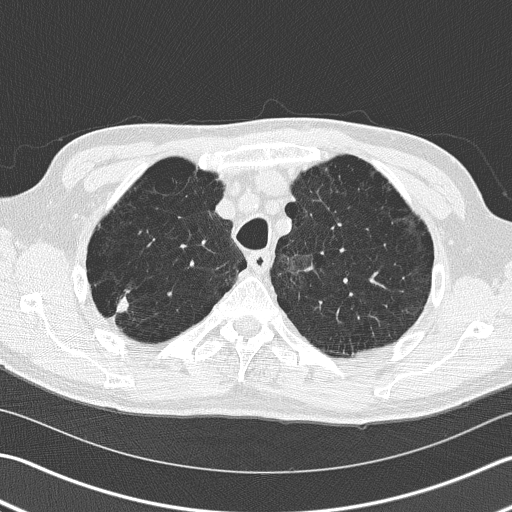
Low-dose screening chest CT, one axial slice. Slice 127 of 163 in the series (ordered by position). 120 kVp. Lung window (W 1500 / L -600 HU). 2 mm slice thickness. 512 × 512 image matrix, field of view 346 × 346 mm.
Structures marked on this image (manually delineated by an expert):
- lesion 1 (tumor, upper lobe of right lung): bounding box (x1, y1, x2, y2) in pixels: (117, 298, 129, 314)